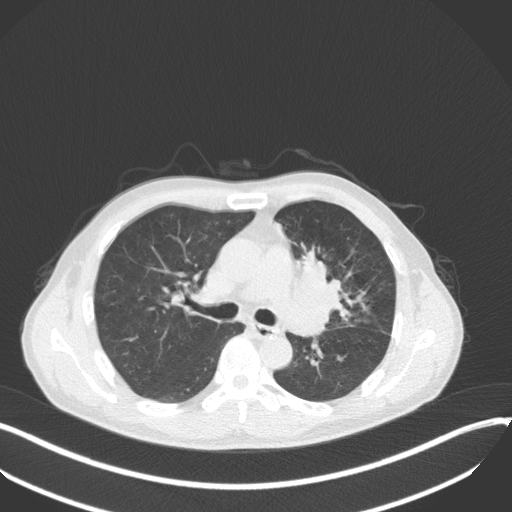
Chest CT, one axial slice. Reconstruction kernel B31f. 120 kVp. Lung window (W 1500 / L -600 HU). 1 mm slice thickness. 512 × 512 image matrix, field of view 400 × 400 mm. Male patient, age 56 years. Case-level facts recorded for this patient, not image findings: clinical TNM (as recorded): T2a N0 M0.
Annotated regions visible in this slice (rectangle marked by the reading radiologist):
- lung tumour (recorded histology: squamous cell carcinoma): bounding box [x1, y1, x2, y2] px = [290, 243, 342, 325]